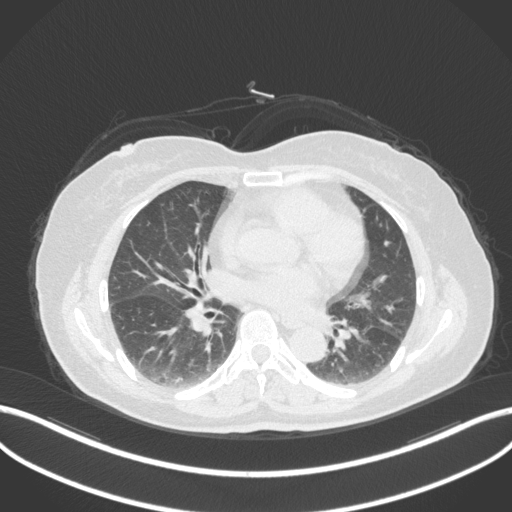
Chest CT, one axial slice. Reconstruction kernel B31f. 120 kVp. Lung window (W 1500 / L -600 HU). 1 mm slice thickness. 512 × 512 image matrix. Female patient, age 59 years. From the clinical record (not read from this slice): clinical TNM (as recorded): T2a N0 M0; histopathological grade: G2-3.
Structures marked on this image (rectangle marked by the reading radiologist):
- lung tumour (recorded histology: adenocarcinoma): box from (x=352, y=326) to (x=373, y=350) px